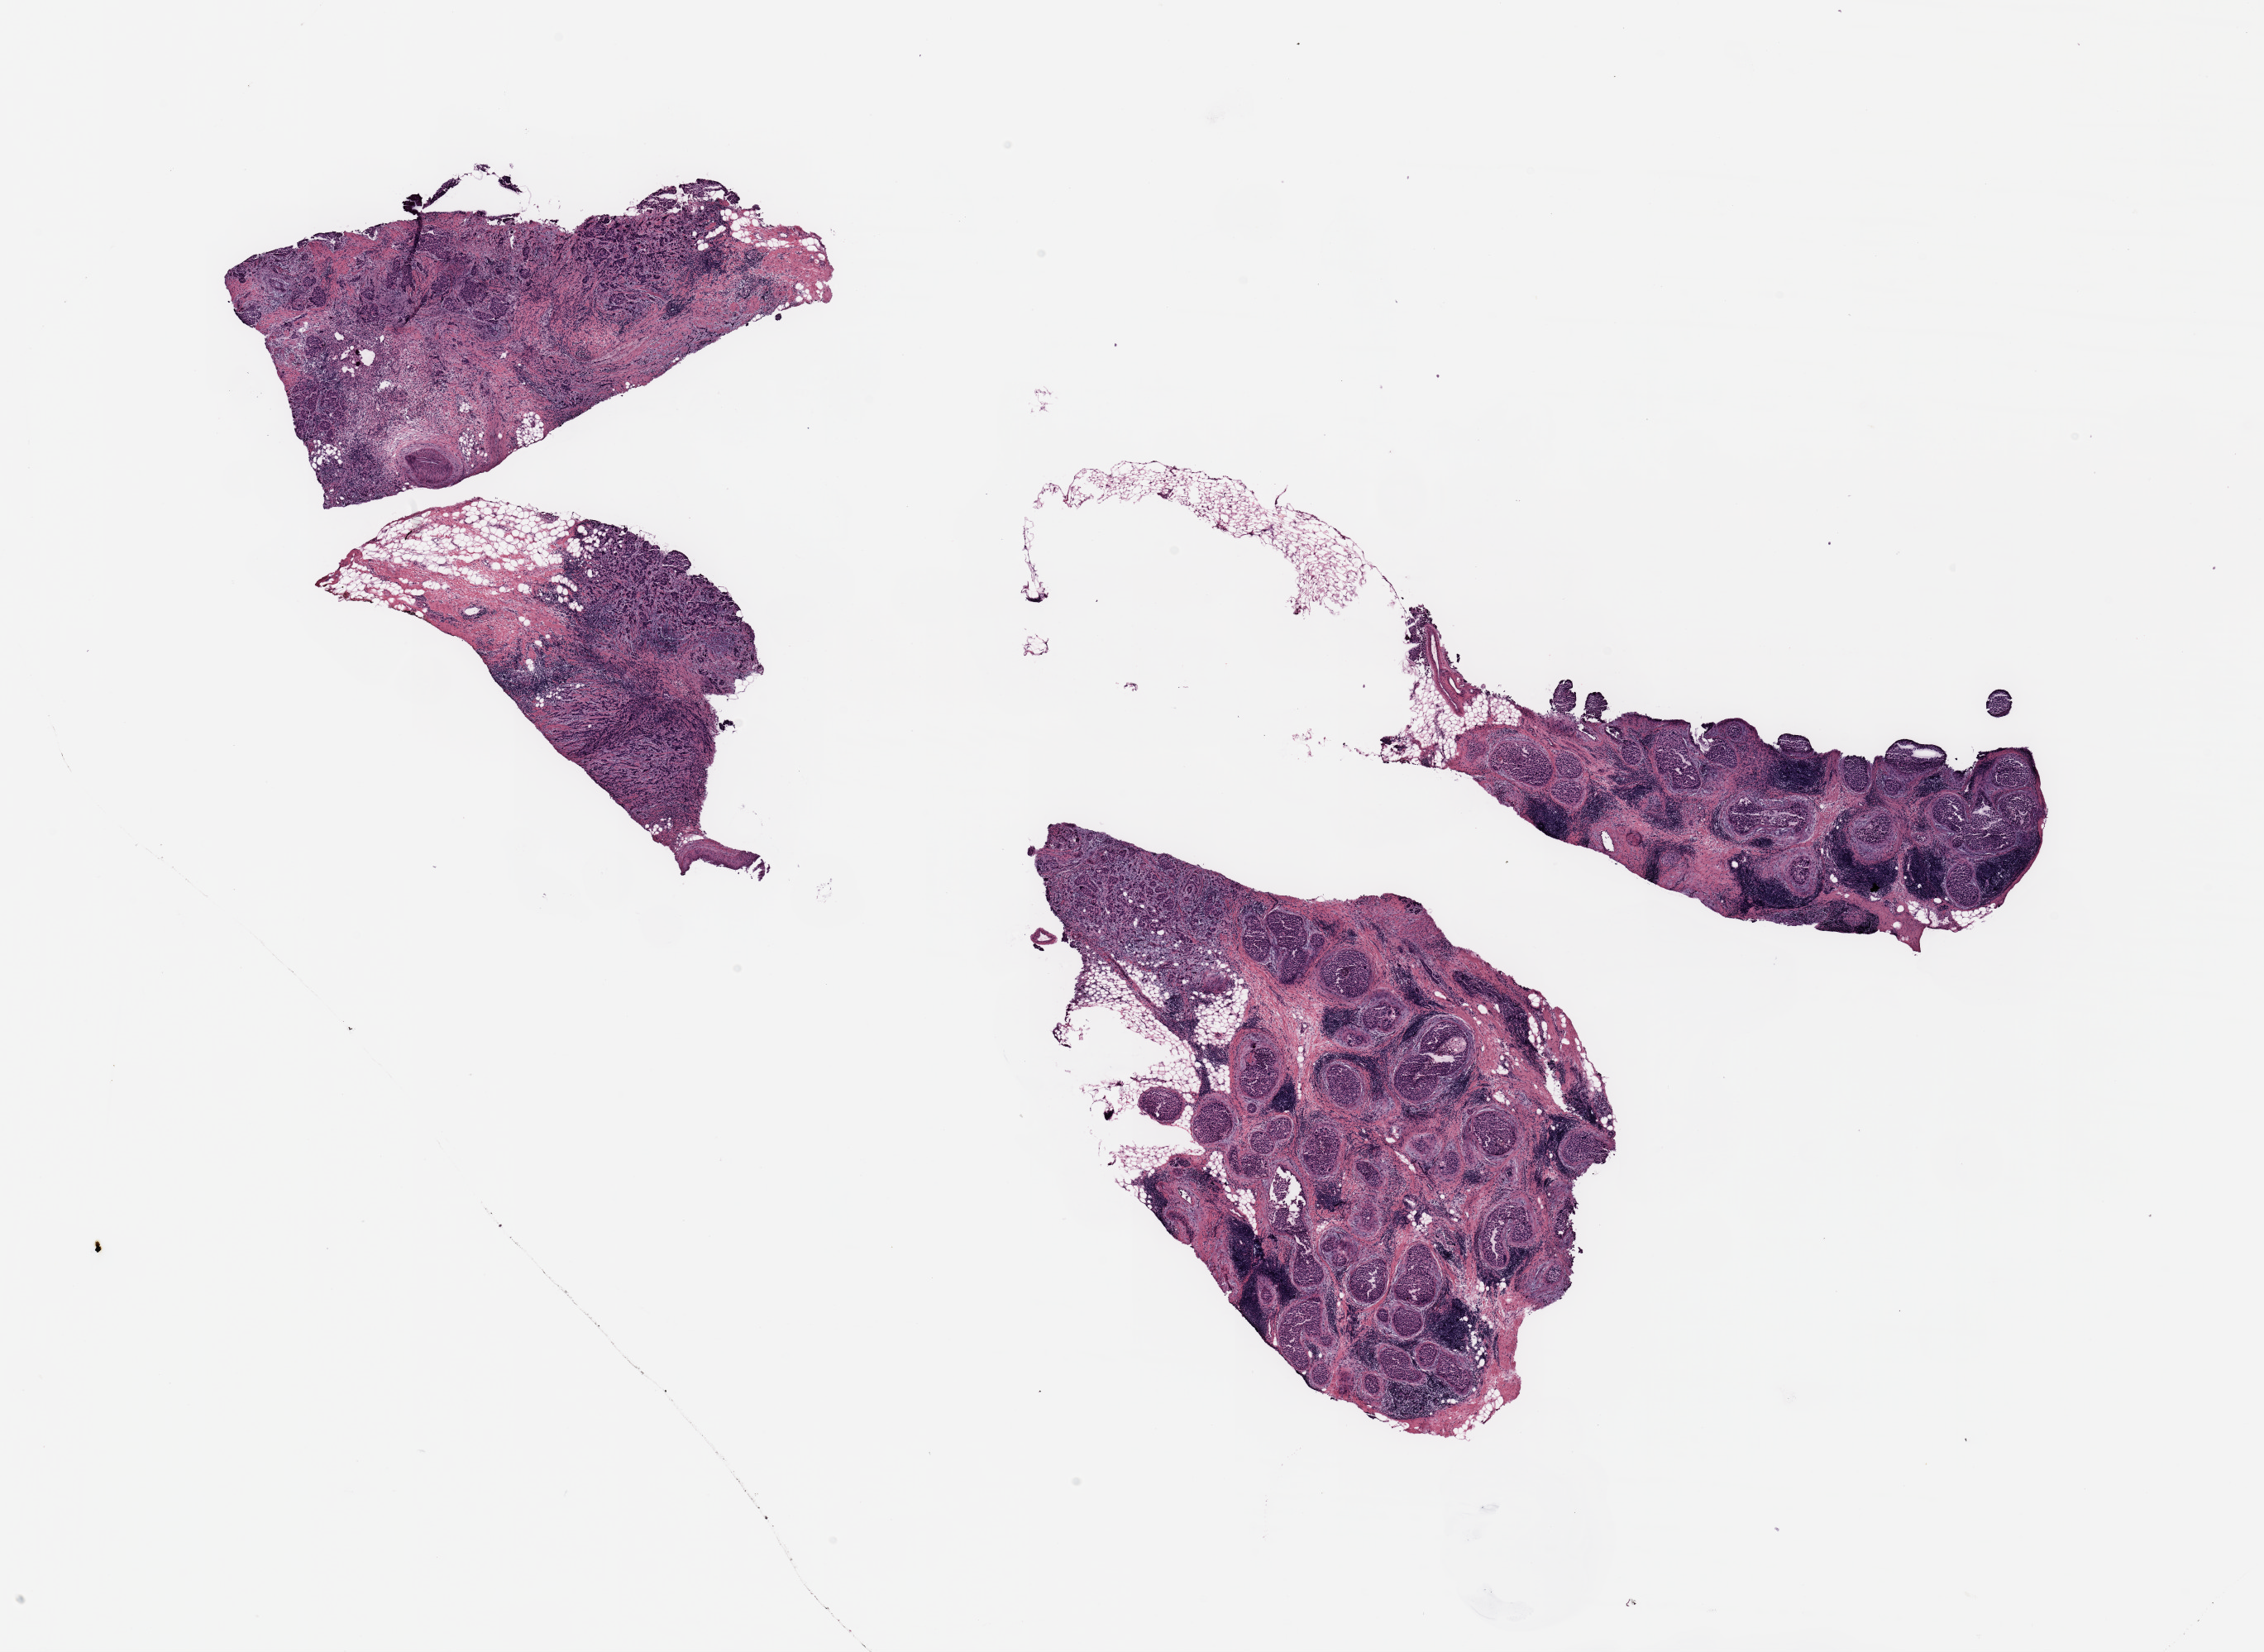
Digitized H&E tissue section (whole slide) — shown as a low-resolution overview of the whole scanned area (about 21.7 x 15.8 mm), breast, tissue type not recorded.
Patient diagnosis (cohort enrolment): breast cancer (breast).